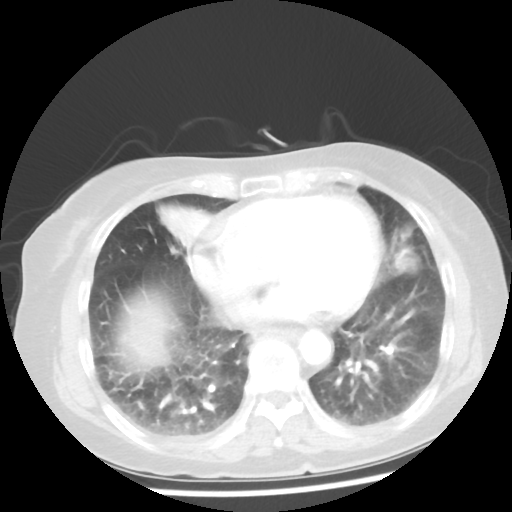
Chest CT, one axial slice. Position 16 of 50 along the scan axis. Lung window (W 1500 / L -600 HU). 5 mm slice thickness. 512 × 512 image matrix, field of view 332 × 332 mm. Female patient, age 77 years. From the clinical record (not read from this slice): clinical TNM (as recorded): T2 N3 M1a.
Outlined on this slice (rectangle marked by the reading radiologist):
- lung tumour (recorded histology: adenocarcinoma): bounding box <389,225,423,282> (left, top, right, bottom; pixels)